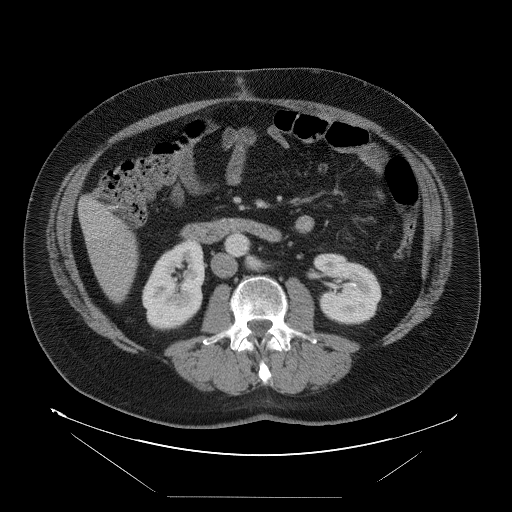
Contrast-enhanced abdominal CT, one axial slice. Slice 24 of 114 in the series (ordered by position). Intravenous contrast given. Soft-tissue window (W 400 / L 40 HU). 5 mm slice thickness. 512 × 512 image matrix. Male patient, age 61 years. Case-level facts recorded for this patient, not image findings: diagnosis: colorectal cancer liver metastases, imaged before liver resection; multiple liver metastases: no; largest metastasis: 6.5 cm; chemotherapy before resection: no.
Outlined on this slice (expert manual segmentation):
- liver: box from (x=80, y=197) to (x=138, y=303) px